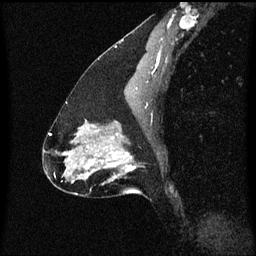
Breast MRI (dynamic contrast-enhanced), one sagittal slice; position 37 of 60 along the scan axis; dynamic contrast-enhanced series, image 2 of 3 at this slice position (ordered by acquisition); 1.5 T; TE 4.2 ms, TR 8.4 ms; 2 mm slice thickness; 256 × 256 image matrix, field of view 200 × 200 mm. Patient: female, 47 years.
Structures marked on this image (semi-automatically segmented with operator editing):
- analysis volume of interest (the breast-tissue region the enhancement analysis was run in; not a lesion): bounding box (x1, y1, x2, y2) in pixels: (85, 136, 144, 195)
- tumour enhancement mask (voxels above the 70 % enhancement threshold inside the analysis volume of interest): (85, 138, 137, 173)